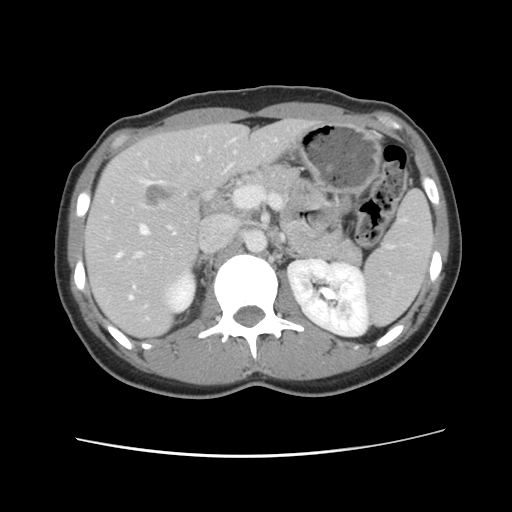
Contrast-enhanced abdominal CT, one axial slice; 120 kVp; soft-tissue window (W 400 / L 40 HU); 512 × 512 image matrix. Female patient, age 33 years. Case-level facts recorded for this patient, not image findings: diagnosis: colorectal cancer liver metastases, imaged before liver resection; multiple liver metastases: yes; largest metastasis: 4.5 cm.
Annotated regions visible in this slice (expert manual segmentation):
- hepatic veins: bounding box <117,157,201,300> (left, top, right, bottom; pixels)
- liver: <87,120,315,337>
- planned liver remnant (the part of the liver to remain after resection): <87,120,315,337>
- portal vein (with intrahepatic branches): <133,225,177,259>
- liver metastasis: <143,182,179,210>